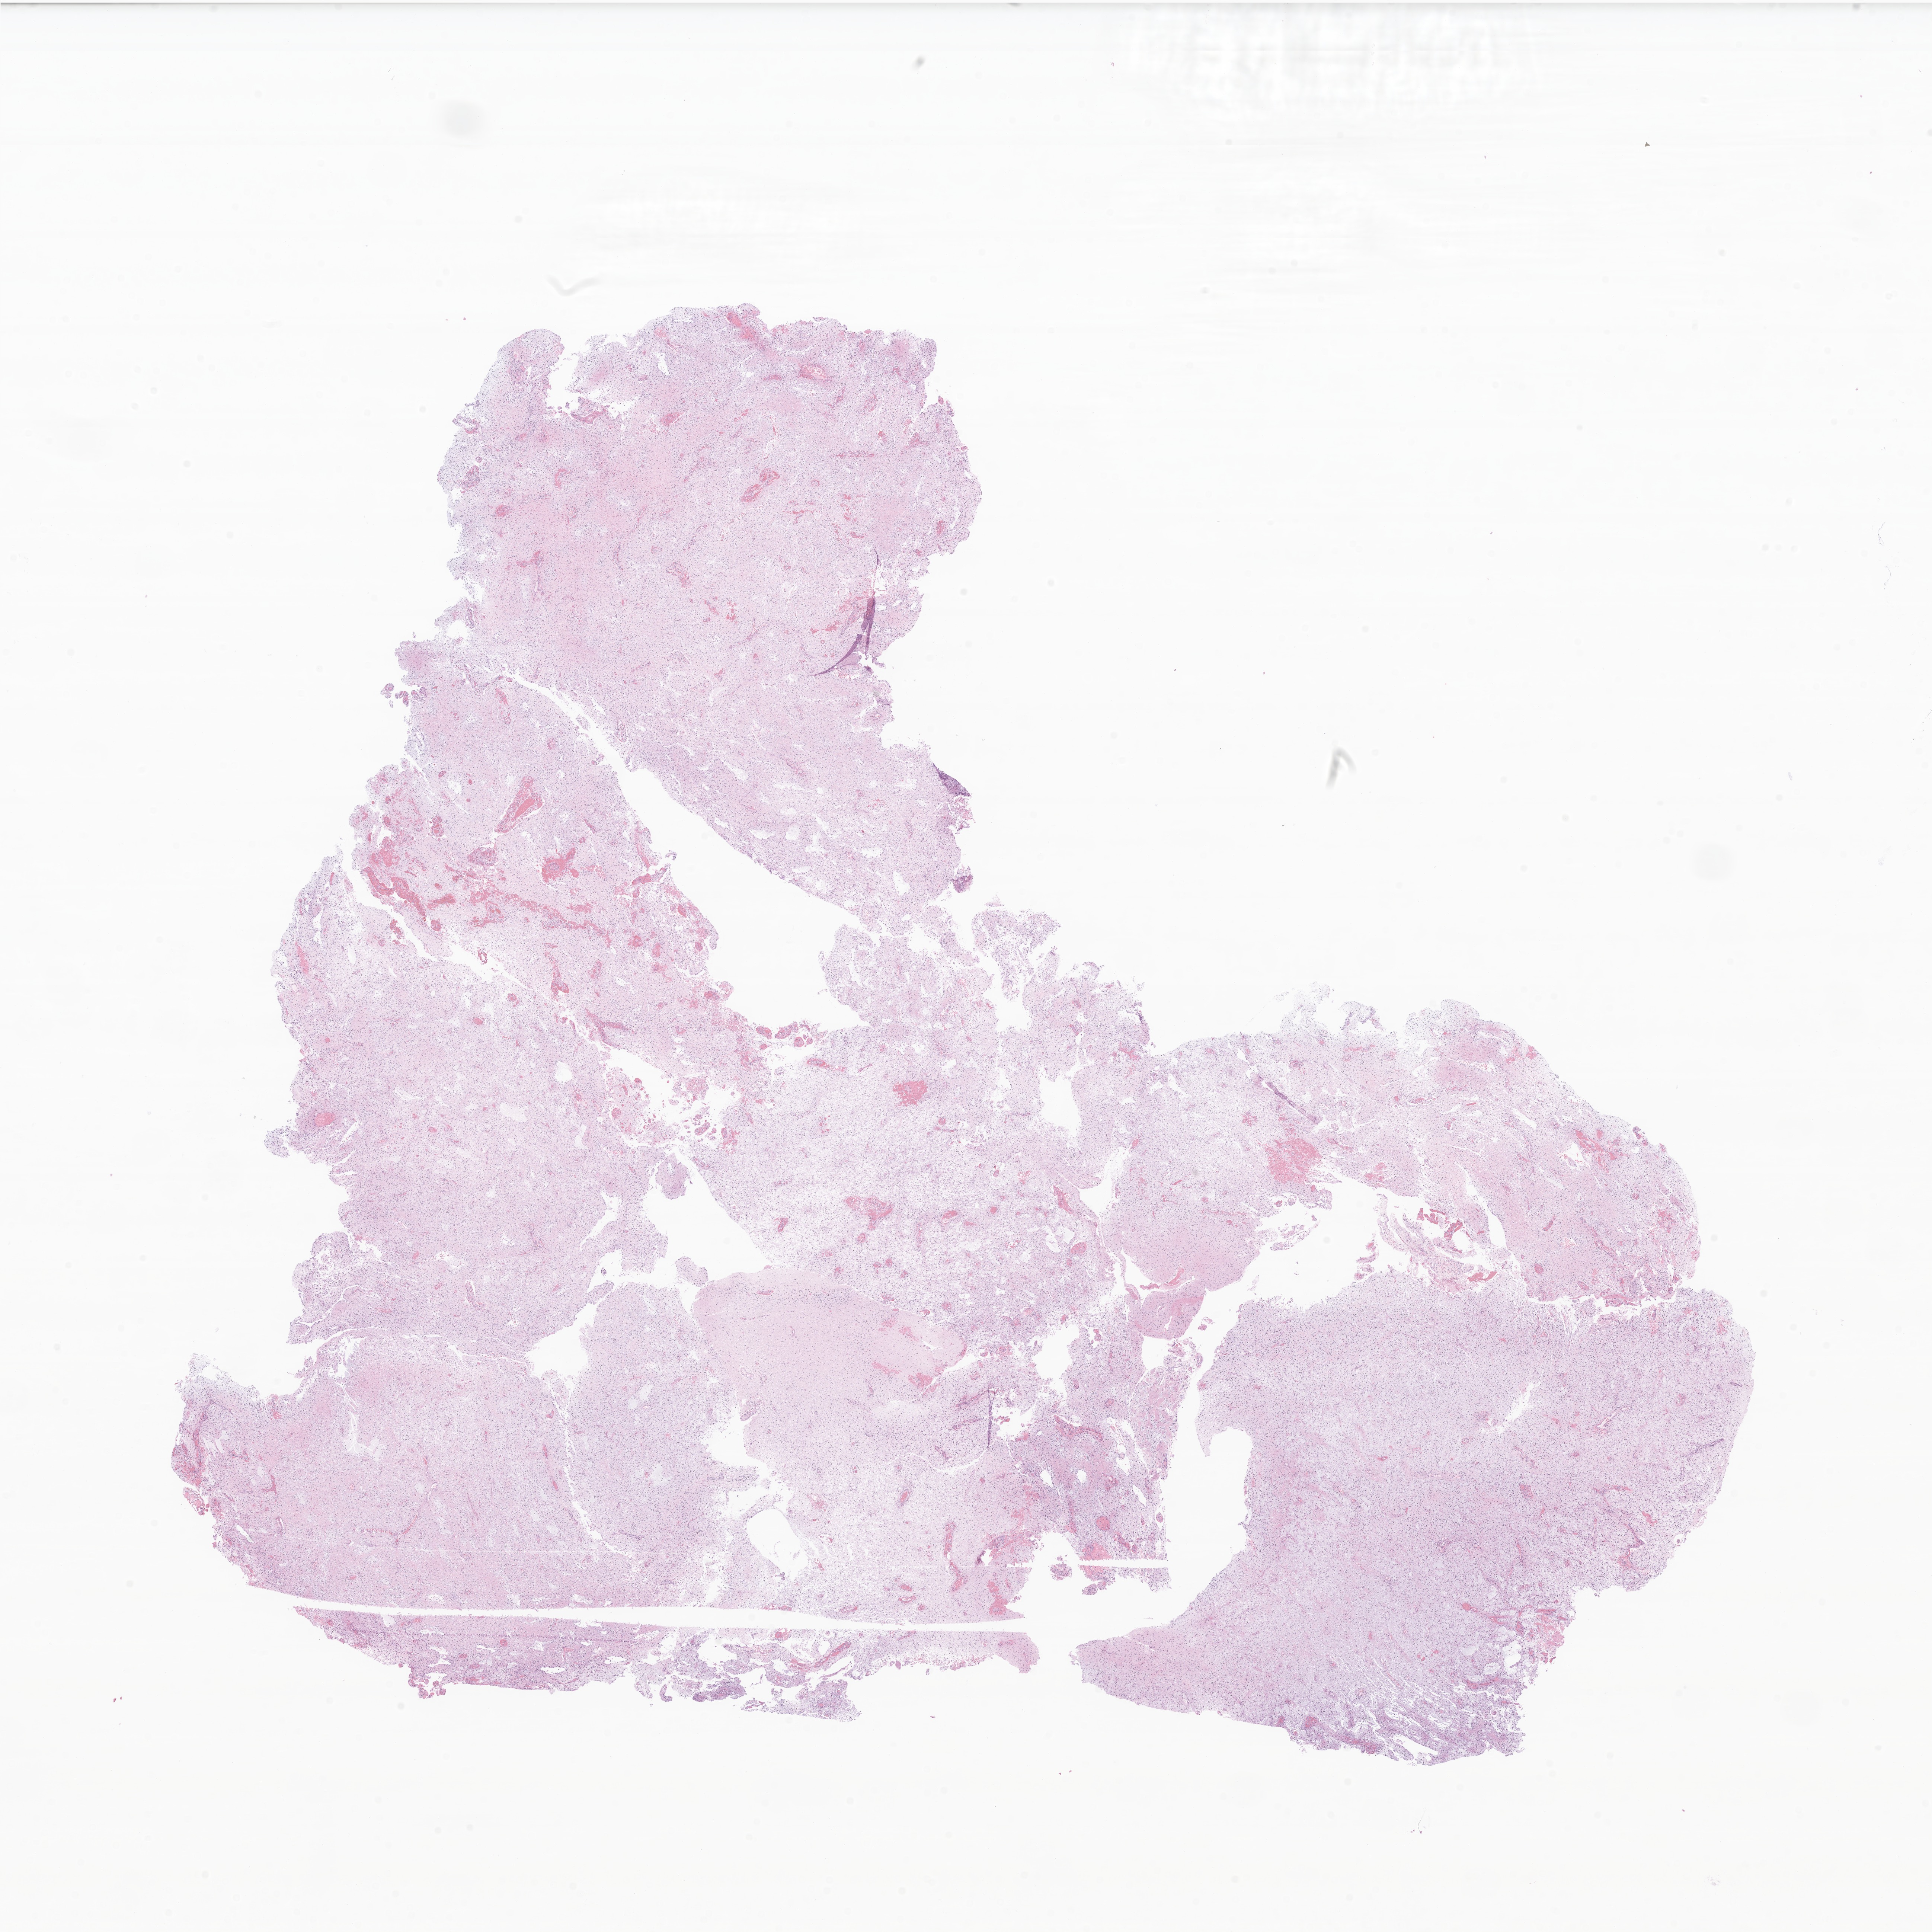
Haematoxylin and eosin whole-slide image of tumor tissue from the brain — shown as a low-resolution overview of the whole scanned area (about 21.9 x 21.9 mm). FFPE section. Patient male; age 115 months (9 years 7 months).
Diagnosis: Pilocytic astrocytoma.